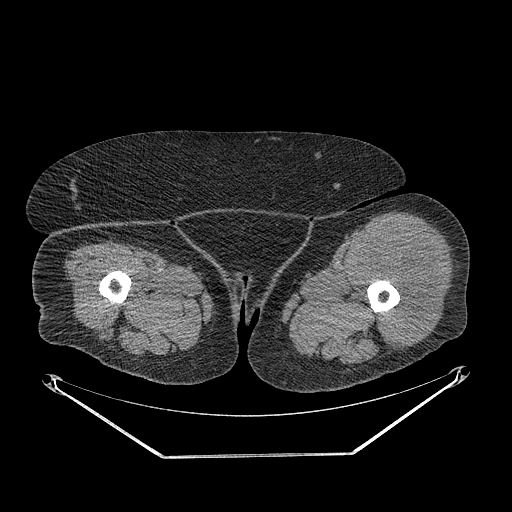
CT of an extremity soft-tissue mass (from a PET/CT study), one axial slice. Slice 244 of 267 in the series (ordered by position). 140 kVp. Soft-tissue window (W 400 / L 40 HU). 3.75 mm slice thickness. 512 × 512 image matrix, field of view 500 × 500 mm. Female patient. From the clinical record (not read from this slice): histological type: undifferentiated – high grade; grade: high; site of the primary tumour: left thigh.
Outlined on this slice (expert contour drawn on MRI and transferred to this co-registered scan by the dataset authors):
- gross tumour volume including surrounding oedema: bounding box <354,231,437,350> (left, top, right, bottom; pixels)
- gross tumour volume (mass): <356,237,437,350>